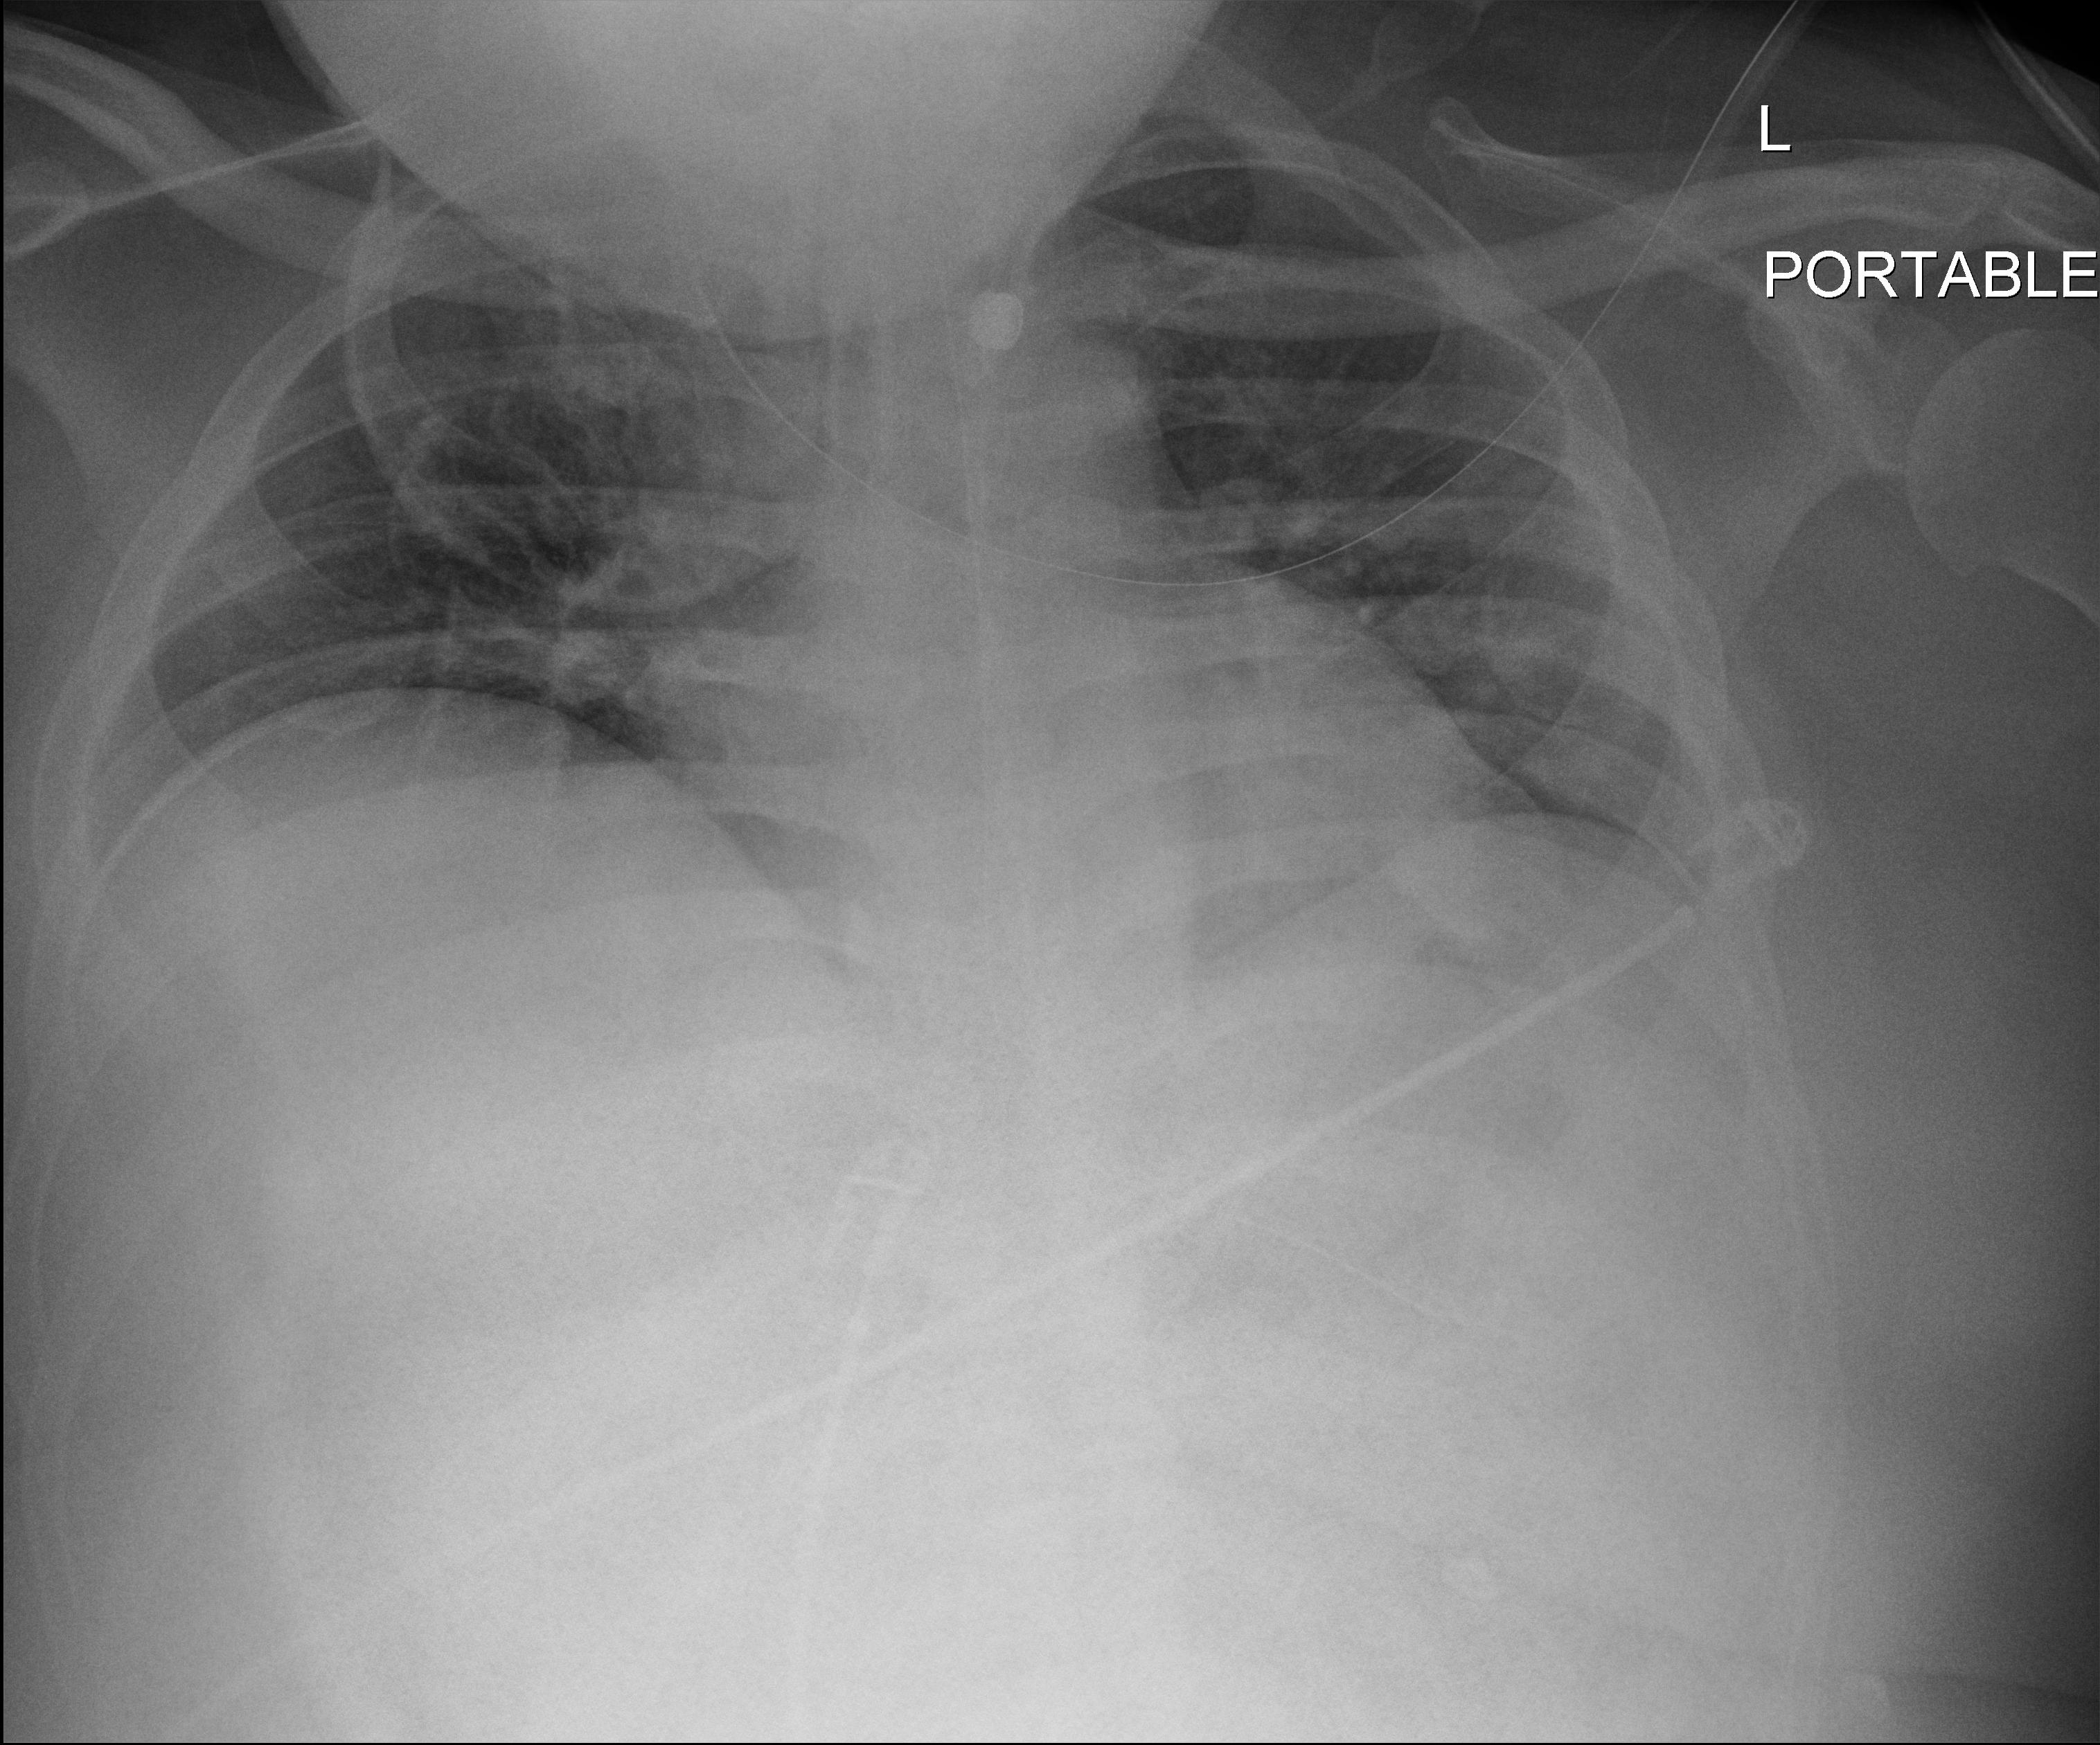
Portable chest radiograph; anteroposterior (AP) projection. Patient hospitalised with COVID-19; male, aged 18–59 years.
From the hospital-stay record, not from the radiograph (when in the stay this image was taken is not recorded): smoking status (admission record): never.